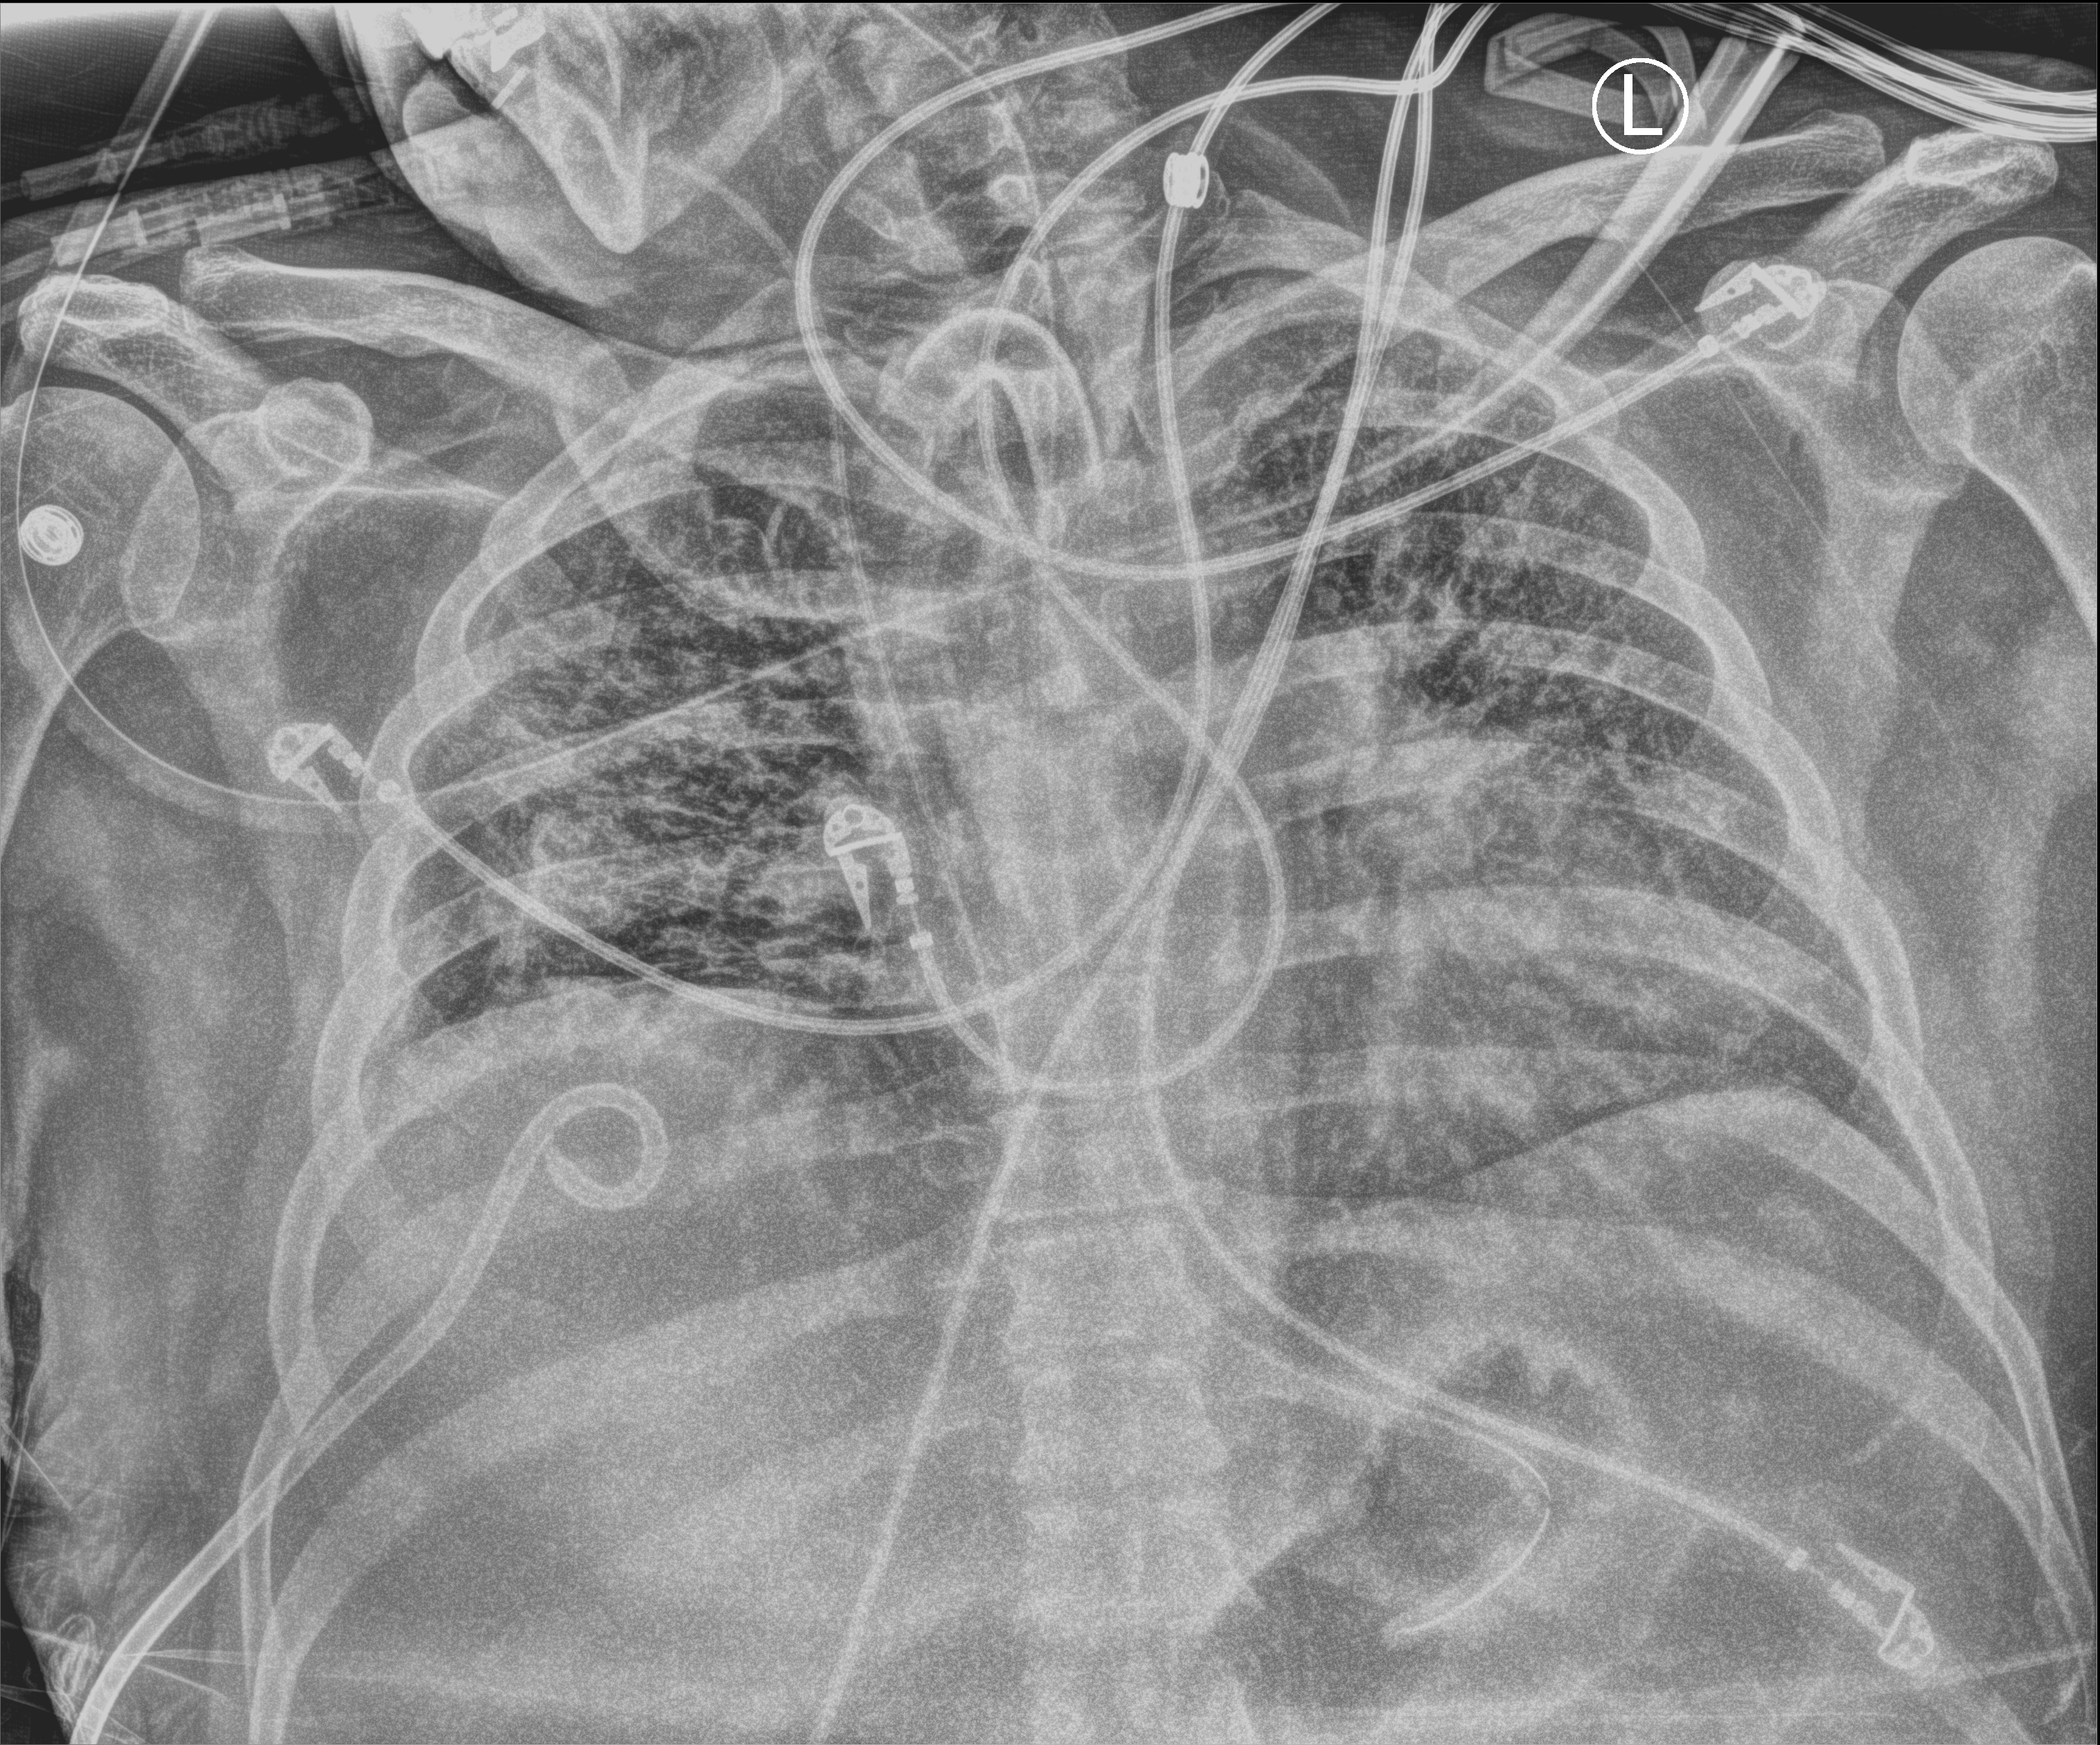
Portable chest radiograph; anteroposterior (AP) projection. Patient hospitalised with COVID-19; male, aged 18–59 years.
From the hospital-stay record, not from the radiograph (when in the stay this image was taken is not recorded):
- hypertension (admission record): yes
- mechanically ventilated during this hospital stay: yes
- admitted to intensive care during this hospital stay: yes